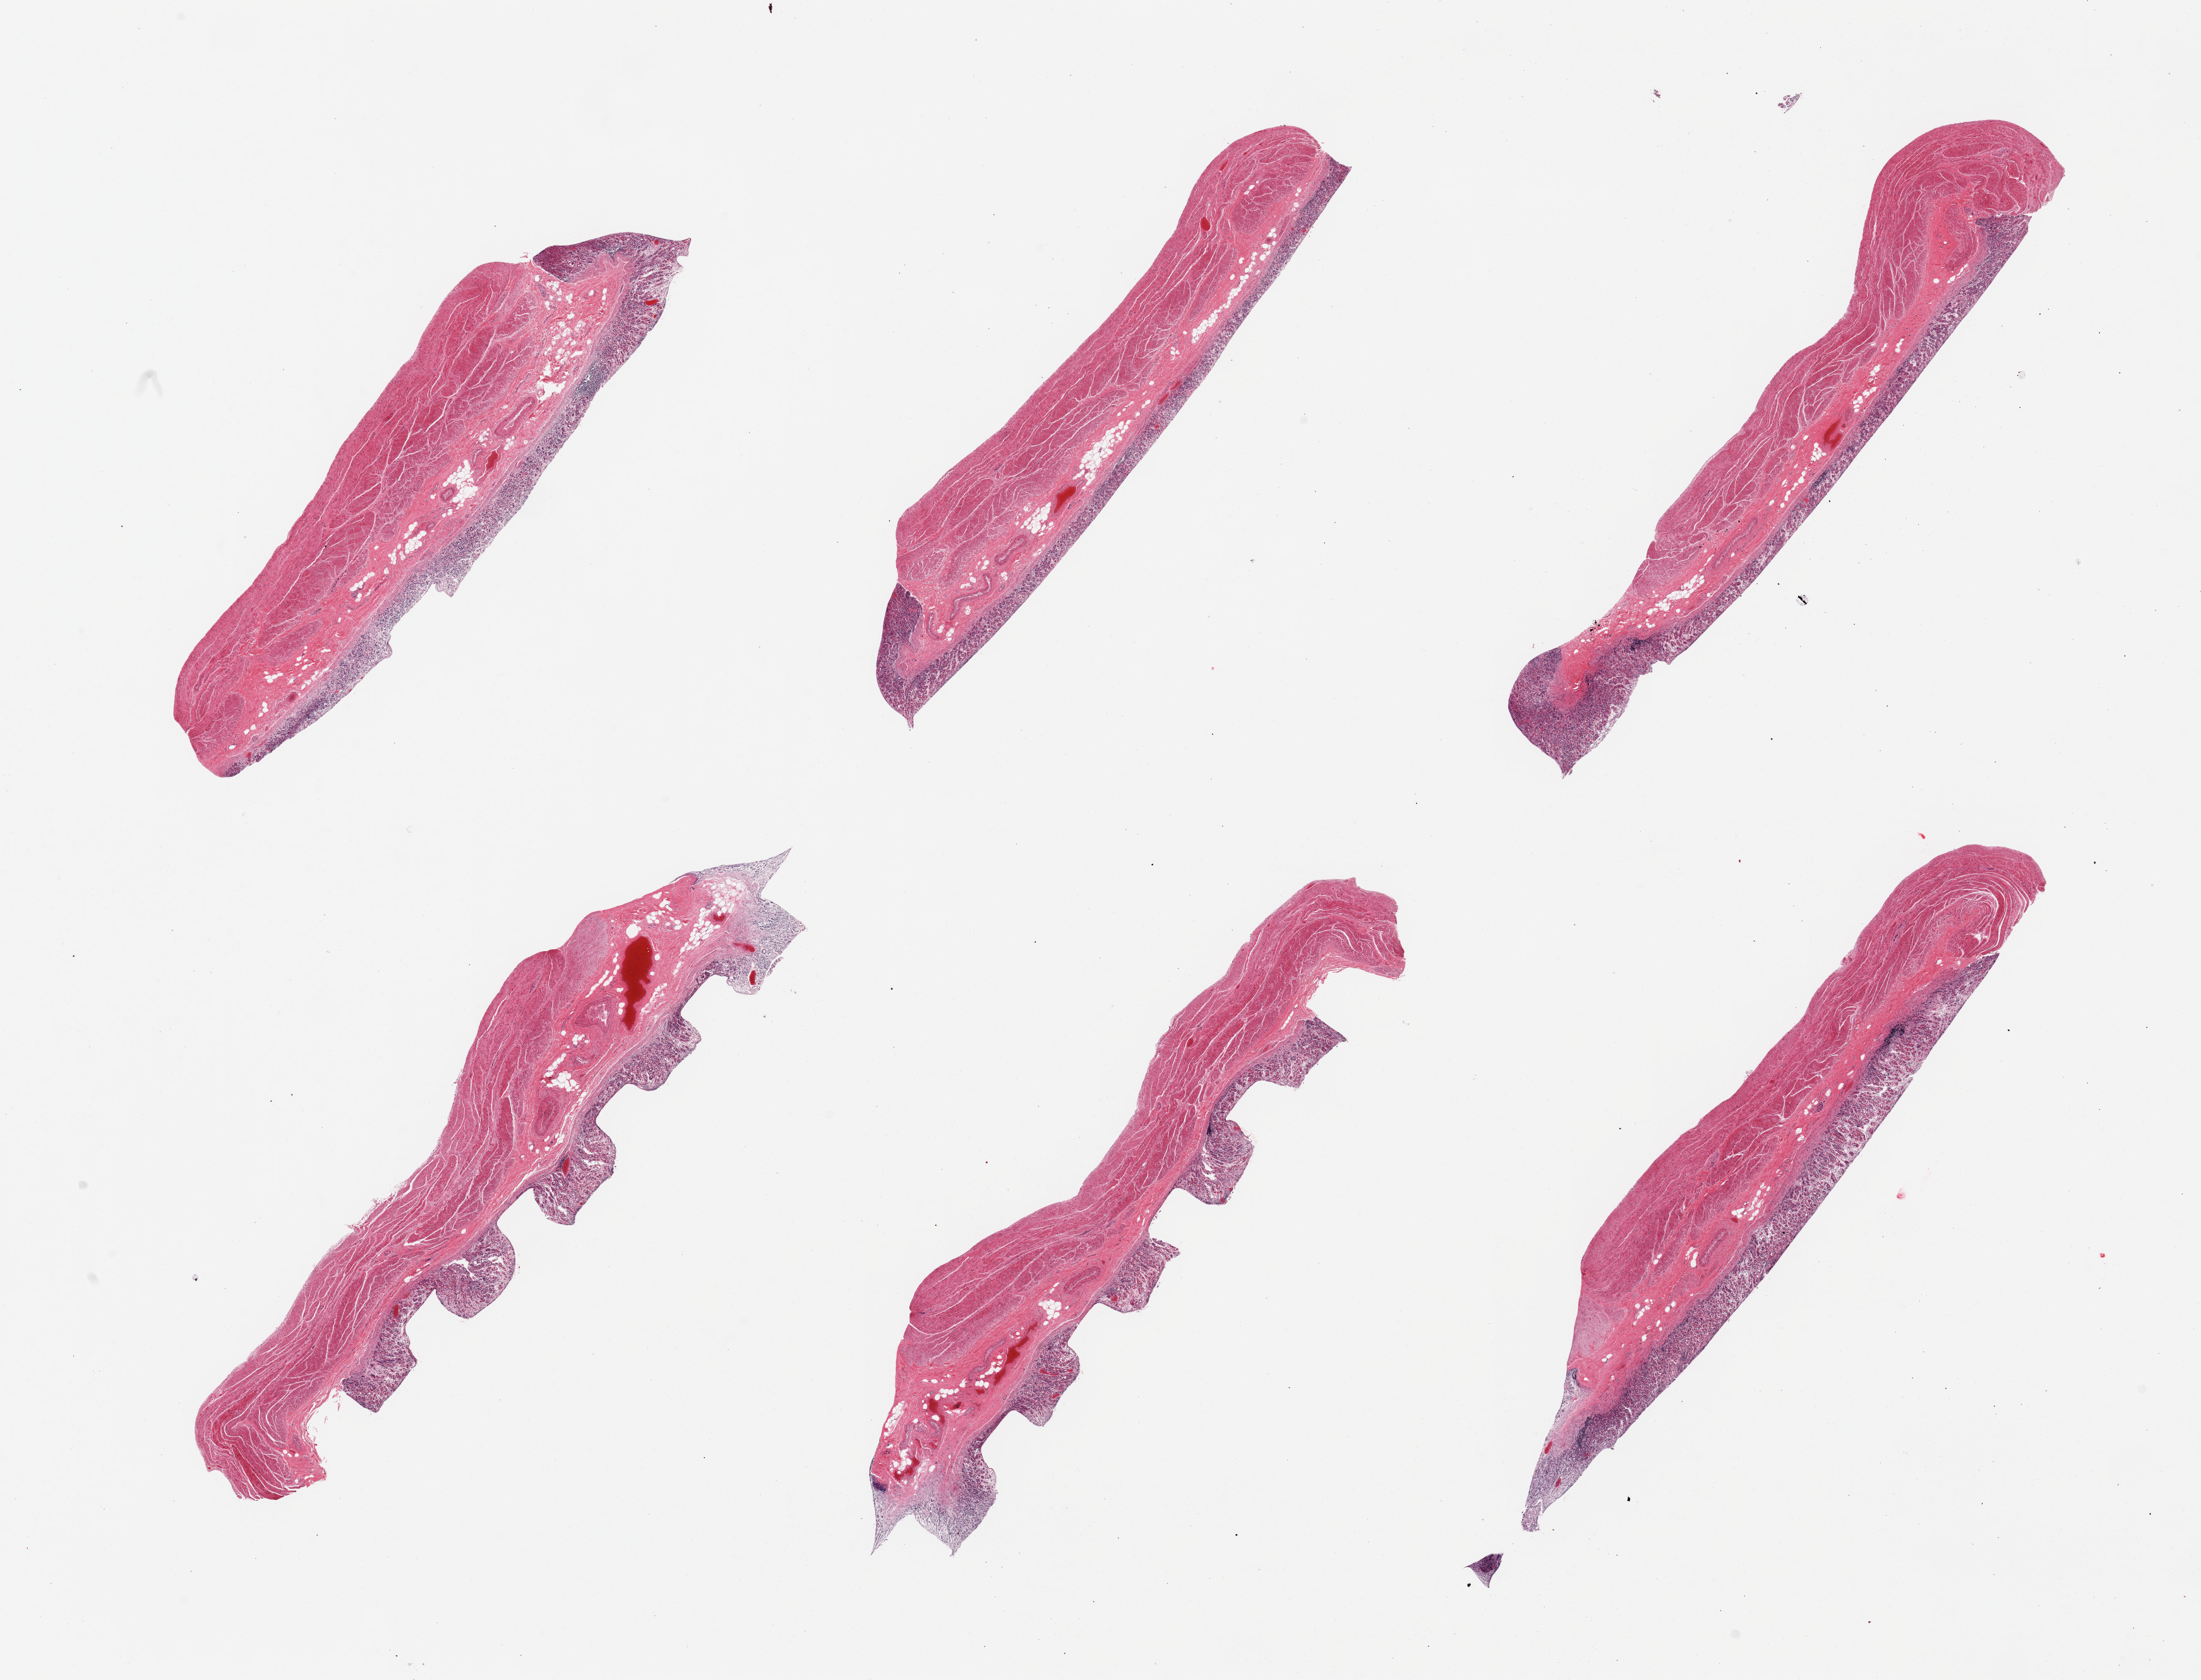
Hematoxylin and eosin (H&E) whole-slide image — low-resolution overview of the scanned area, about 27.6 x 21.0 mm, PAXgene-fixed, paraffin-embedded tissue, target tissue: stomach, donor tissue sample. Donor sex: male.
Review note (as recorded): 6 pieces; full thickness sections, moderatly autolyzed mucosa.